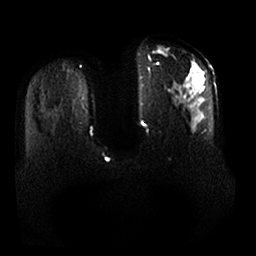
Breast MRI, one axial slice; slice 10 of 25 in the series (ordered by position); diffusion-weighted series; image 2 of 4 stored at this slice position (different b-values; order by instance number); 1.5 T; 4 mm slice thickness; 256 × 256 image matrix, field of view 380 × 380 mm. Female patient.
Outlined on this slice (expert manual segmentation):
- tumour on diffusion-weighted imaging: bounding box [x1, y1, x2, y2] px = [189, 73, 204, 87]